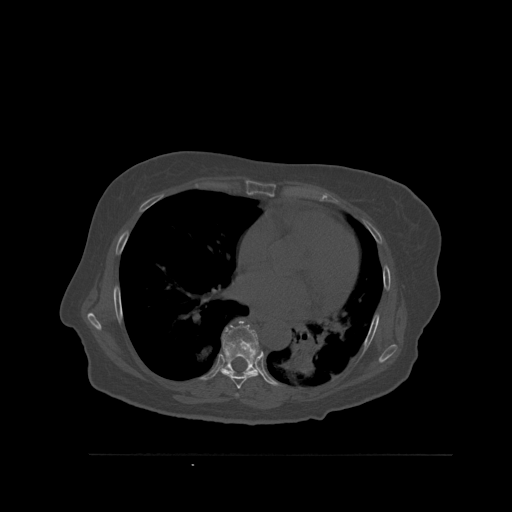
CT including the spine, one axial slice. Slice 359 of 527 in the series (ordered by position). Bone window (W 1800 / L 400 HU). 1.5 mm slice thickness. 512 × 512 image matrix, field of view 470 × 470 mm. Patient: female, 73 years. From the clinical record (not read from this slice): primary cancer: breast.
Annotated regions visible in this slice (semi-automatic segmentation, software-assisted and operator-edited):
- T6 vertebra: bounding box <235,393,239,397> (left, top, right, bottom; pixels)
- T7 vertebra: <221,351,261,389>
- T8 vertebra: <222,321,259,373>